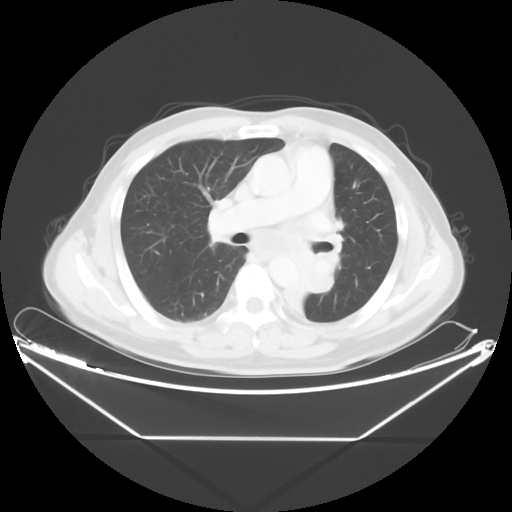
Chest CT, one axial slice; position 27 of 48 along the scan axis; reconstruction kernel STANDARD; lung window (W 1500 / L -600 HU); 5 mm slice thickness; 512 × 512 image matrix. Male patient, age 58 years. Case-level facts recorded for this patient, not image findings: clinical TNM (as recorded): T3 N3 M0.
Structures marked on this image (rectangle marked by the reading radiologist):
- lung tumour (recorded histology: squamous cell carcinoma): bounding box [x1, y1, x2, y2] px = [278, 250, 341, 327]